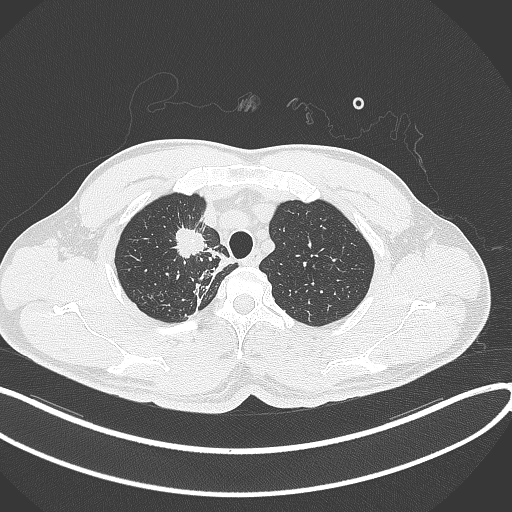
Chest CT, one axial slice; slice 317 of 391 in the series (ordered by position); 120 kVp; lung window (W 1500 / L -600 HU); 512 × 512 image matrix, field of view 400 × 400 mm. Patient: male, 48 years. Case-level facts recorded for this patient, not image findings: clinical TNM (as recorded): T1c N1 M1.
Structures marked on this image (bounding box drawn by a radiologist):
- lung tumour (recorded histology: adenocarcinoma): bounding box [x1, y1, x2, y2] px = [170, 221, 208, 261]